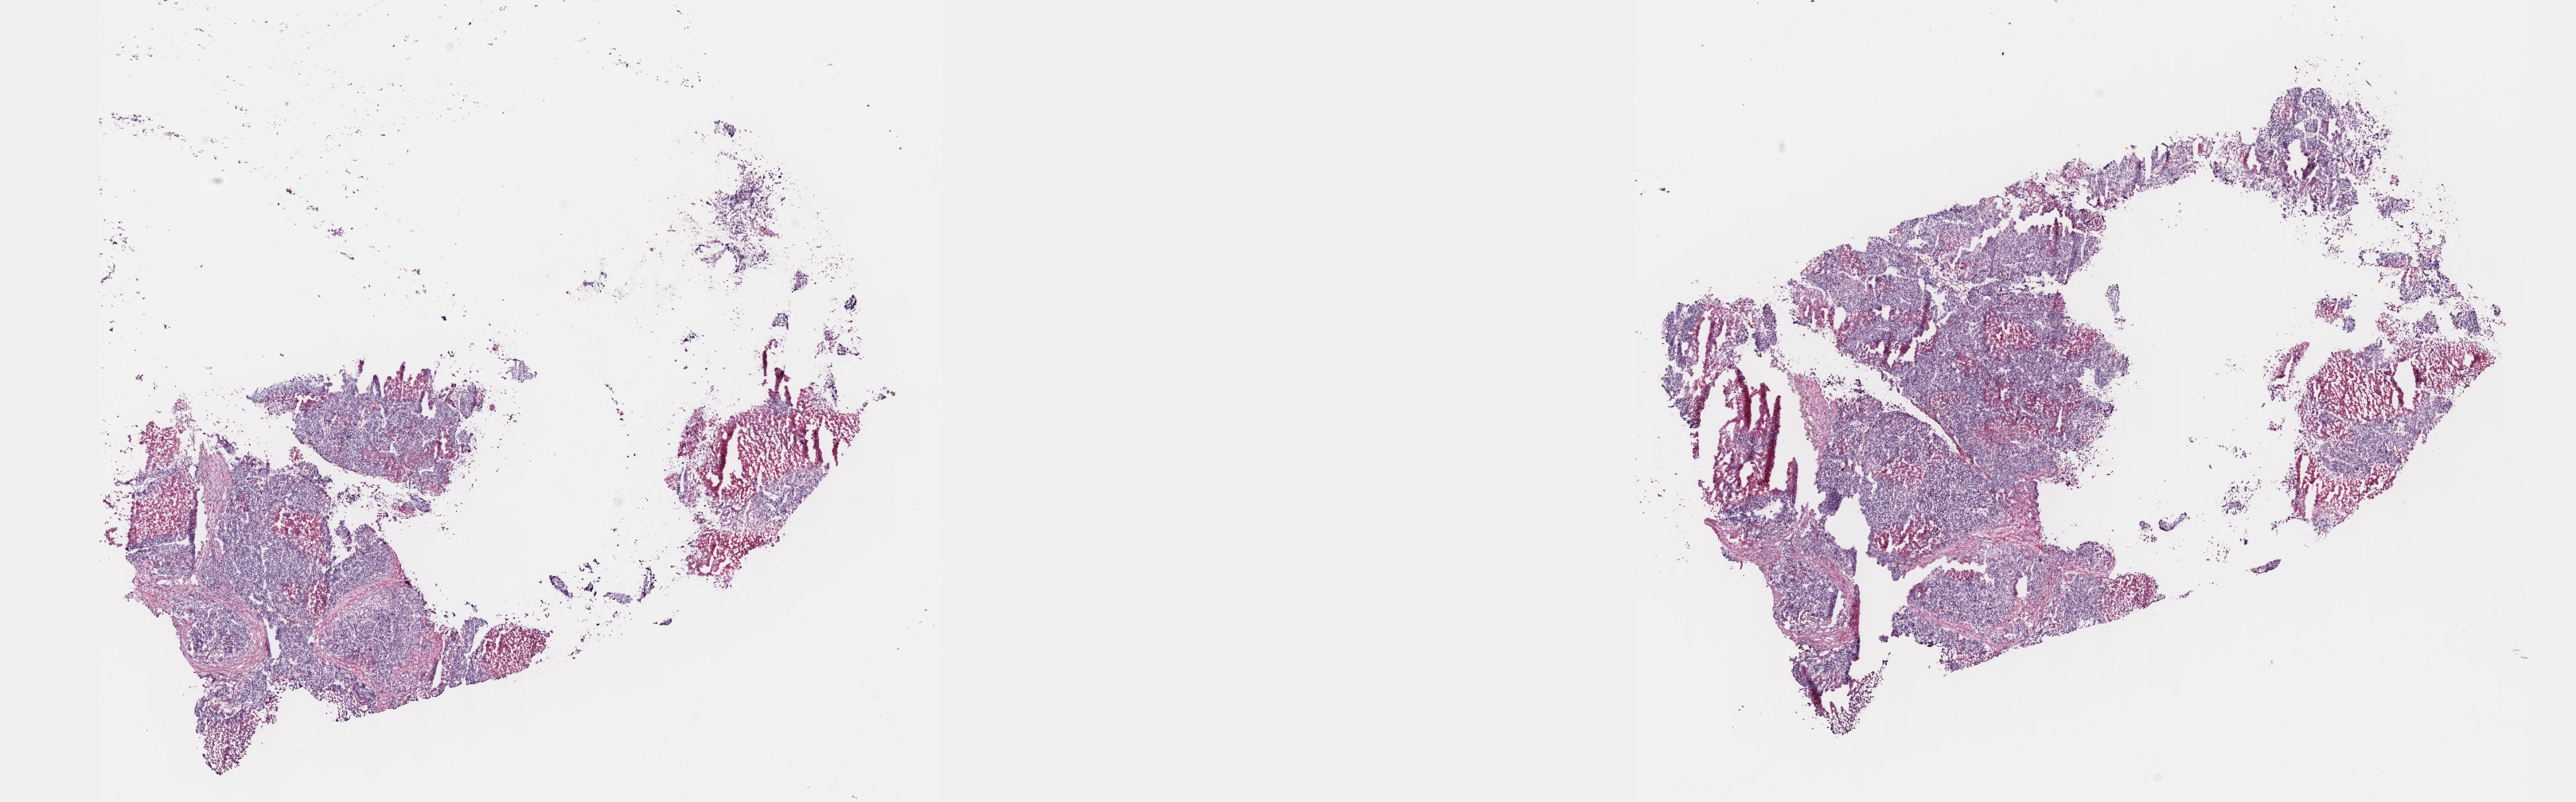
H&E-stained whole-slide image, low-resolution overview of the scanned area, about 26.2 x 8.1 mm. Frozen section from the top of the tissue portion. Liver, primary tumour sample. Patient: male, age at initial diagnosis 70 years. Histologic grade: G2 (moderately differentiated). Pathologist review of this section (percent, as recorded): tumour cells 60%, tumour nuclei 60%, normal cells 0%, stromal cells 20%, necrosis 20%. Inflammatory infiltration, as recorded: lymphocyte infiltration 2%, monocyte infiltration 1%, neutrophil infiltration 1%.
* AJCC pathologic stage: IIIB (7th edition)
* histologic diagnosis: Hepatocellular carcinoma, NOS